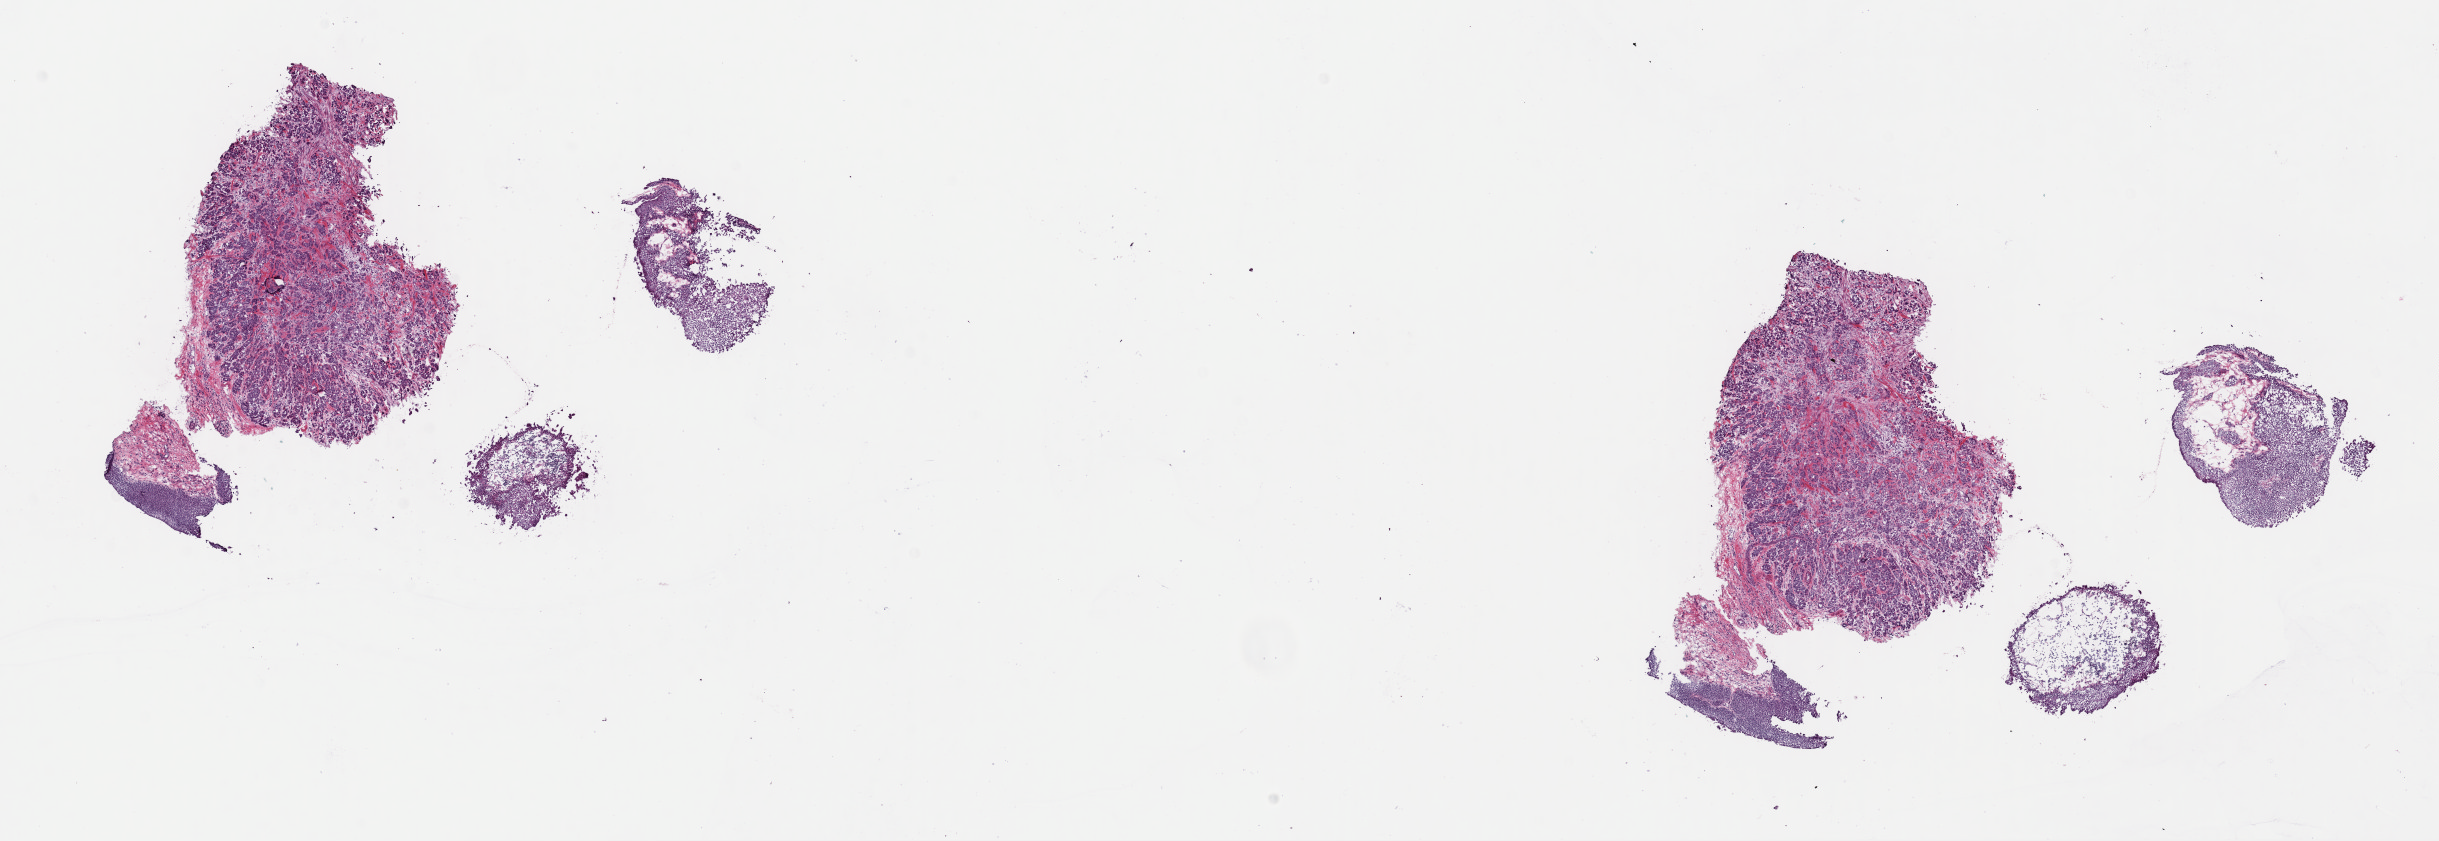
Whole-slide histology image, H&E, shown as a low-resolution overview of the whole scanned area (about 19.3 x 6.6 mm, from a 40x scan). Frozen section from the top of the tissue portion. Sample: primary tumour, bladder. Female patient; age at initial diagnosis 84 years. Histologic grade: high grade. Slide review estimates, as recorded: tumour cells 80%, tumour nuclei 70%, normal cells 10%, stromal cells 10%, necrosis 0%. Infiltration values recorded for this section: lymphocyte infiltration 0%, monocyte infiltration 0%, neutrophil infiltration 0%.
• pathologic diagnosis: Transitional cell carcinoma
• AJCC pathologic stage: IV